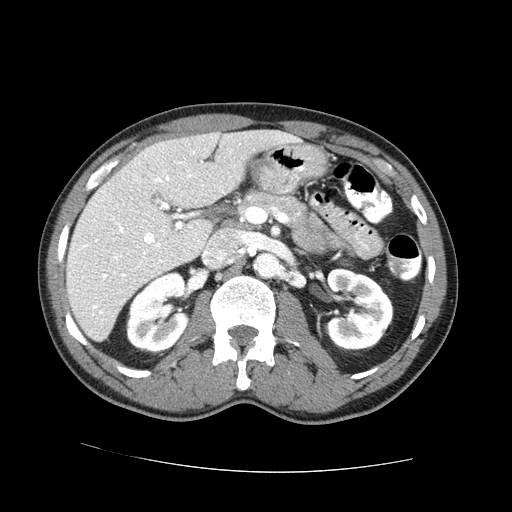
Contrast-enhanced abdominal CT (liver protocol), one axial slice; slice 35 of 73 in the series (ordered by position); 100 kVp; one of 2 acquisitions stored at this slice position; soft-tissue window (W 400 / L 40 HU); 2.5 mm slice thickness; 512 × 512 image matrix. From the clinical record (not read from this slice): diagnosis: hepatocellular carcinoma (patient treated with transarterial chemoembolisation; whether this scan precedes or follows treatment is not stated here); TNM stage (as recorded): Stage-IVA; Child-Pugh class: A; tumour differentiation: no biopsy; tumour nodularity: uninodular.
Annotated regions visible in this slice (semi-automatic segmentation, software-assisted and operator-edited):
- liver parenchyma outside the tumour (the mass and vessels are separate outlines, so this box may not span the whole liver): bounding box <66,130,300,340> (left, top, right, bottom; pixels)
- liver vessels: <83,162,200,314>